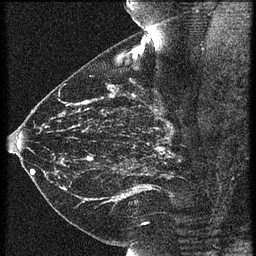
Breast MRI (dynamic contrast-enhanced), one sagittal slice; 3 images stored at this slice position (order not interpretable as contrast timing); 1.5 T; TE 4.2 ms, TR 21.3 ms; 1.5 mm slice thickness; 256 × 256 image matrix. Patient: female, 43 years. Case-level facts recorded for this patient, not image findings: setting: breast cancer imaged before/during neoadjuvant chemotherapy; receptor status: HER2-positive.
Annotated regions visible in this slice (semi-automatic segmentation, software-assisted and operator-edited):
- analysis volume of interest (the breast-tissue region the enhancement analysis was run in; not a lesion): bounding box [x1, y1, x2, y2] px = [119, 114, 189, 173]
- tumour enhancement mask (voxels above the 90 % enhancement threshold inside the analysis volume of interest): [158, 124, 172, 157]